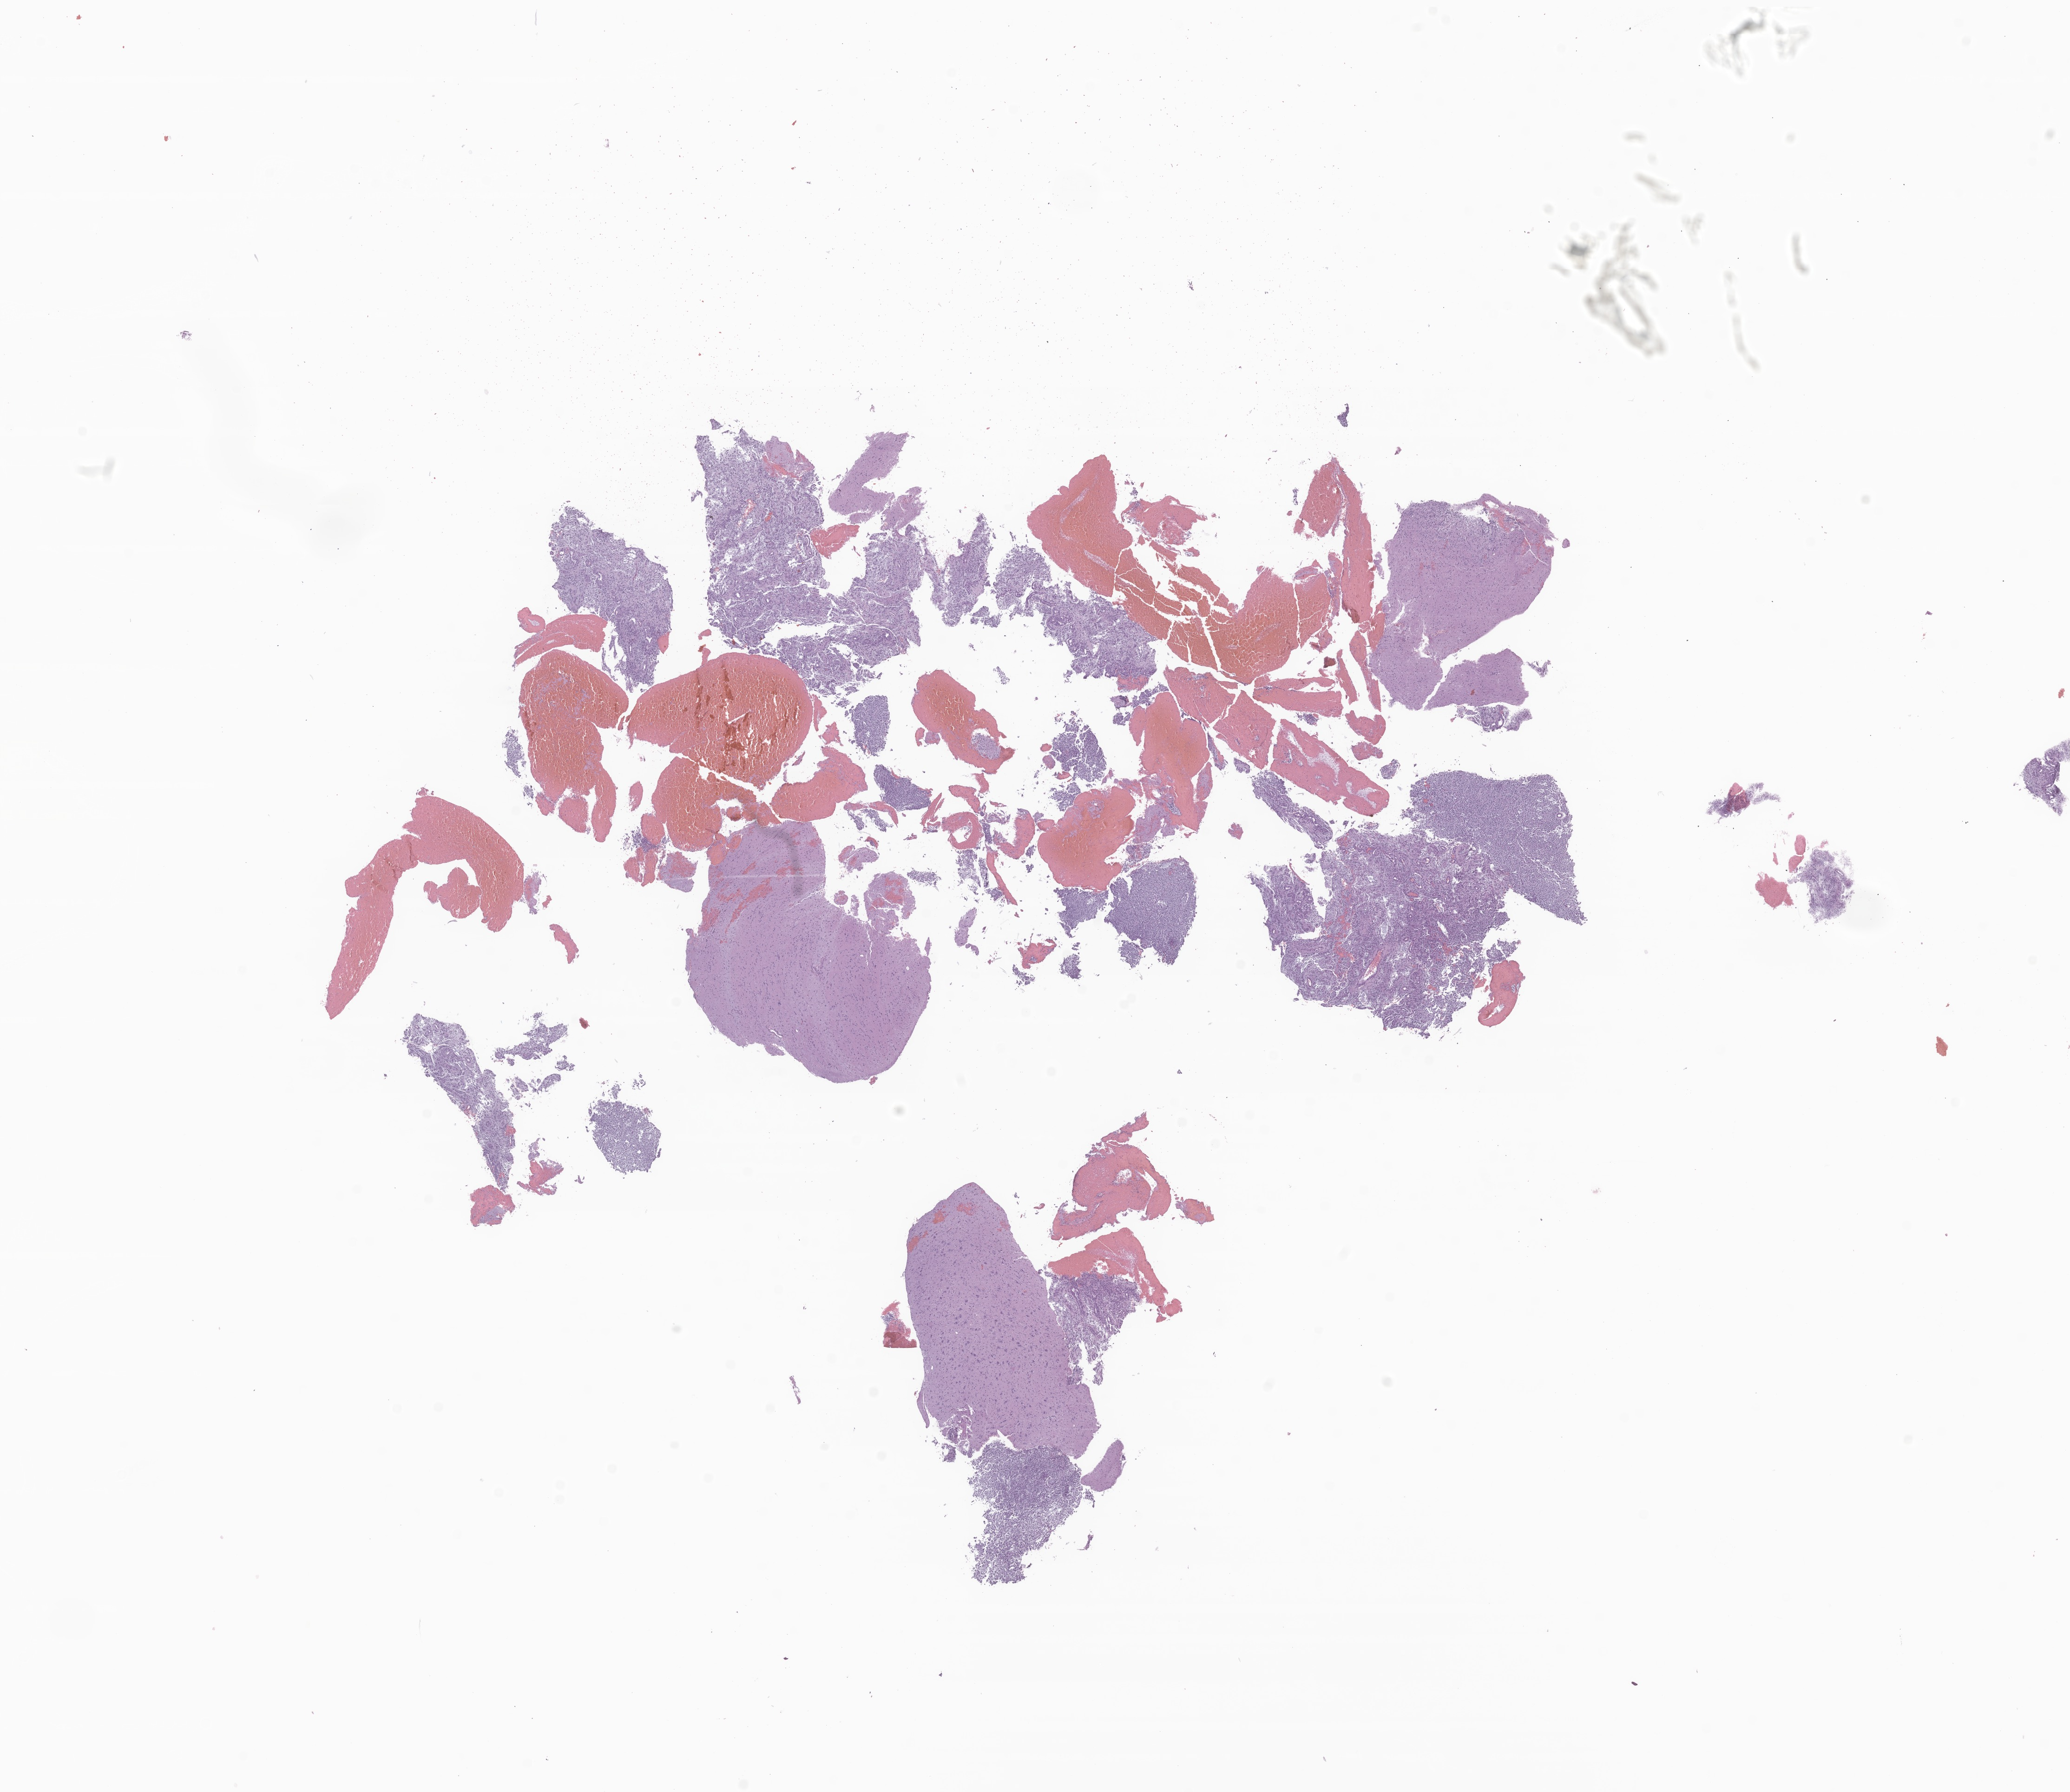
Digitized H&E-stained section of tumor tissue from the brain — low-resolution overview of the scanned area, about 18.8 x 16.3 mm; formalin-fixed paraffin-embedded section. Male patient, age 35 months (2 years 11 months).
Diagnosis: Glioma, malignant.